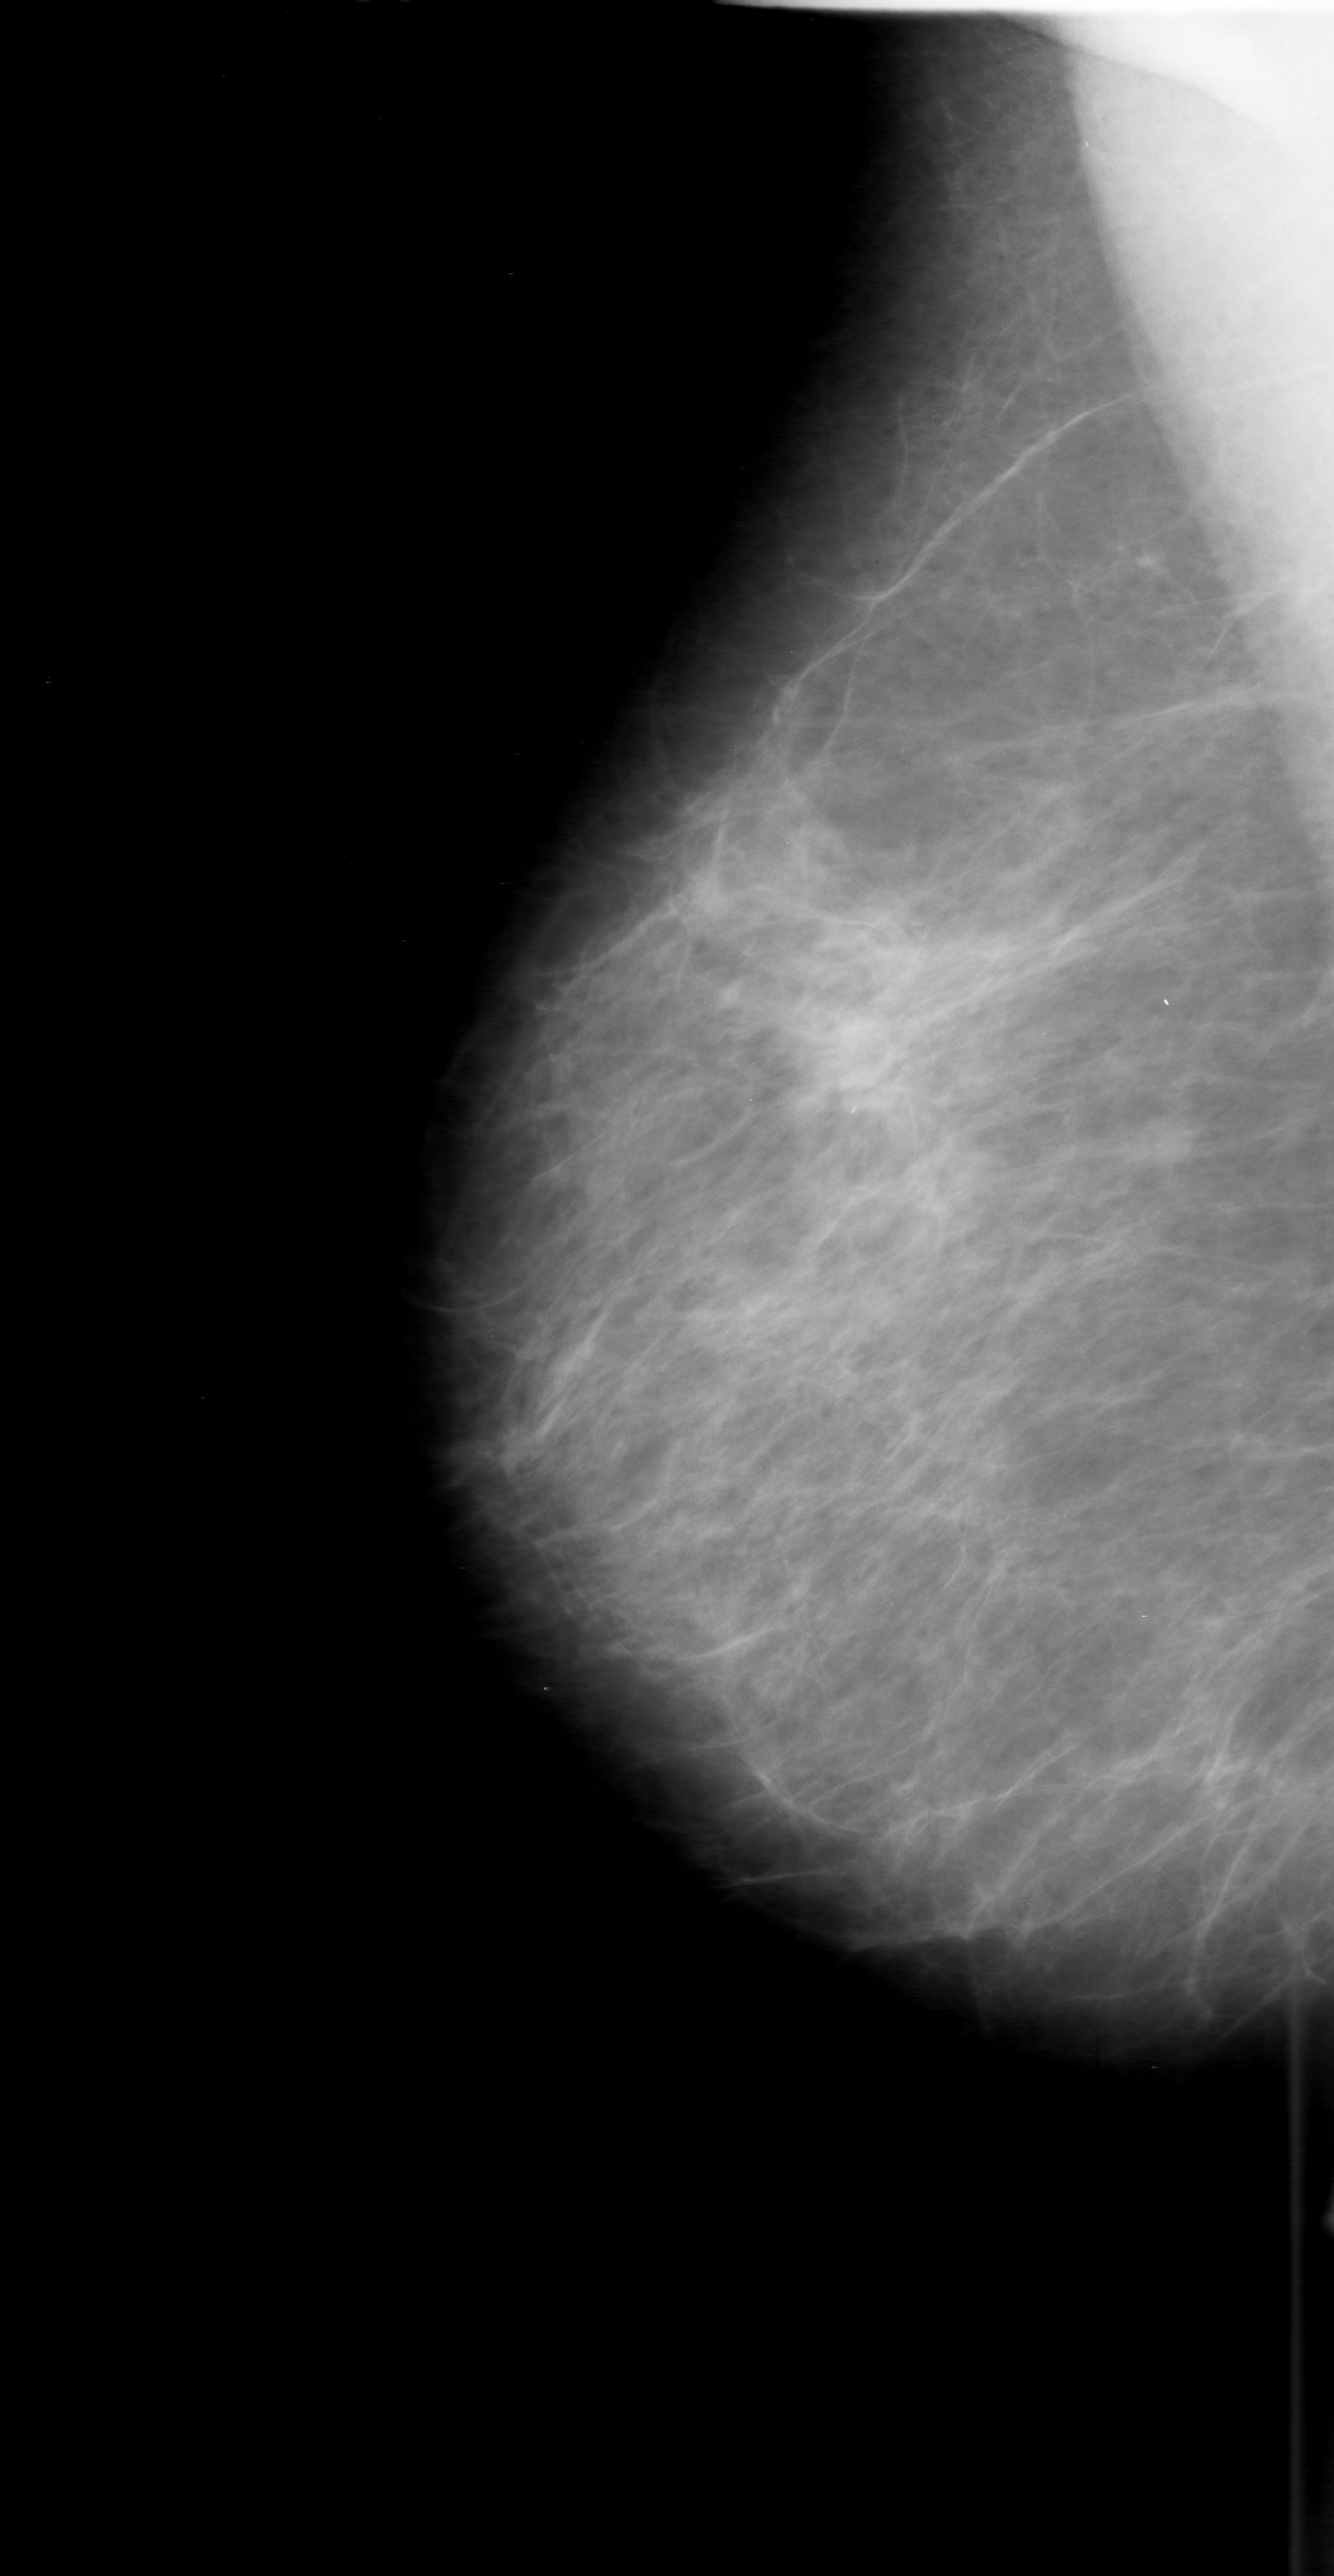
Mammogram (digitized film), right breast, MLO view, breast composition: scattered fibroglandular densities (BI-RADS density category 2 of 4).
Finding: mass, shape irregular, margins obscured; BI-RADS assessment category 3; pathology (as recorded): malignant.